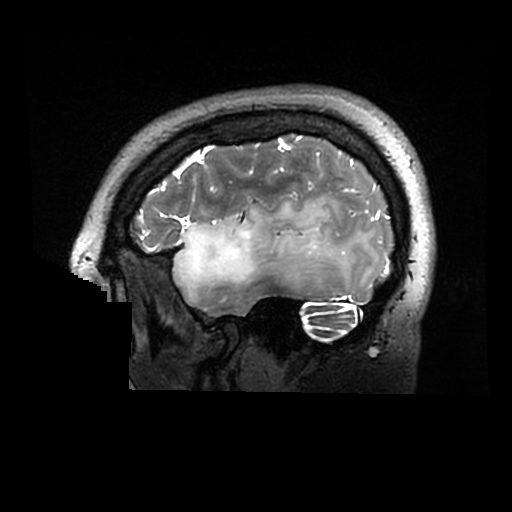
Brain MRI from a brain-tumour surgery series, one sagittal slice; 0.6 mm slice thickness; 512 × 512 image matrix, field of view 240 × 240 mm. From the clinical record (not read from this slice): histopathology: Astrocytoma; WHO grade: 2; IDH mutation: yes.
Annotated regions visible in this slice (outlined manually by an expert reader):
- tumour: bounding box [x1, y1, x2, y2] px = [172, 197, 378, 298]